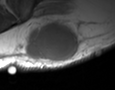
MRI of an extremity soft-tissue mass, one axial slice. Position 21 of 35 along the scan axis. MR volume resampled by the dataset authors to the PET/CT grid (not the native acquisition matrix). 115 × 90 image matrix, field of view 112 × 88 mm. Male patient. Case-level facts recorded for this patient, not image findings: histological type: pleiomorphic leiomyosarcoma; grade: high; site of the primary tumour: left buttock.
Annotated regions visible in this slice (expert contour drawn on MRI and transferred to this co-registered scan by the dataset authors):
- gross tumour volume including surrounding oedema: box from (x=26, y=21) to (x=81, y=61) px
- gross tumour volume (mass): (x=26, y=23)–(x=79, y=61)